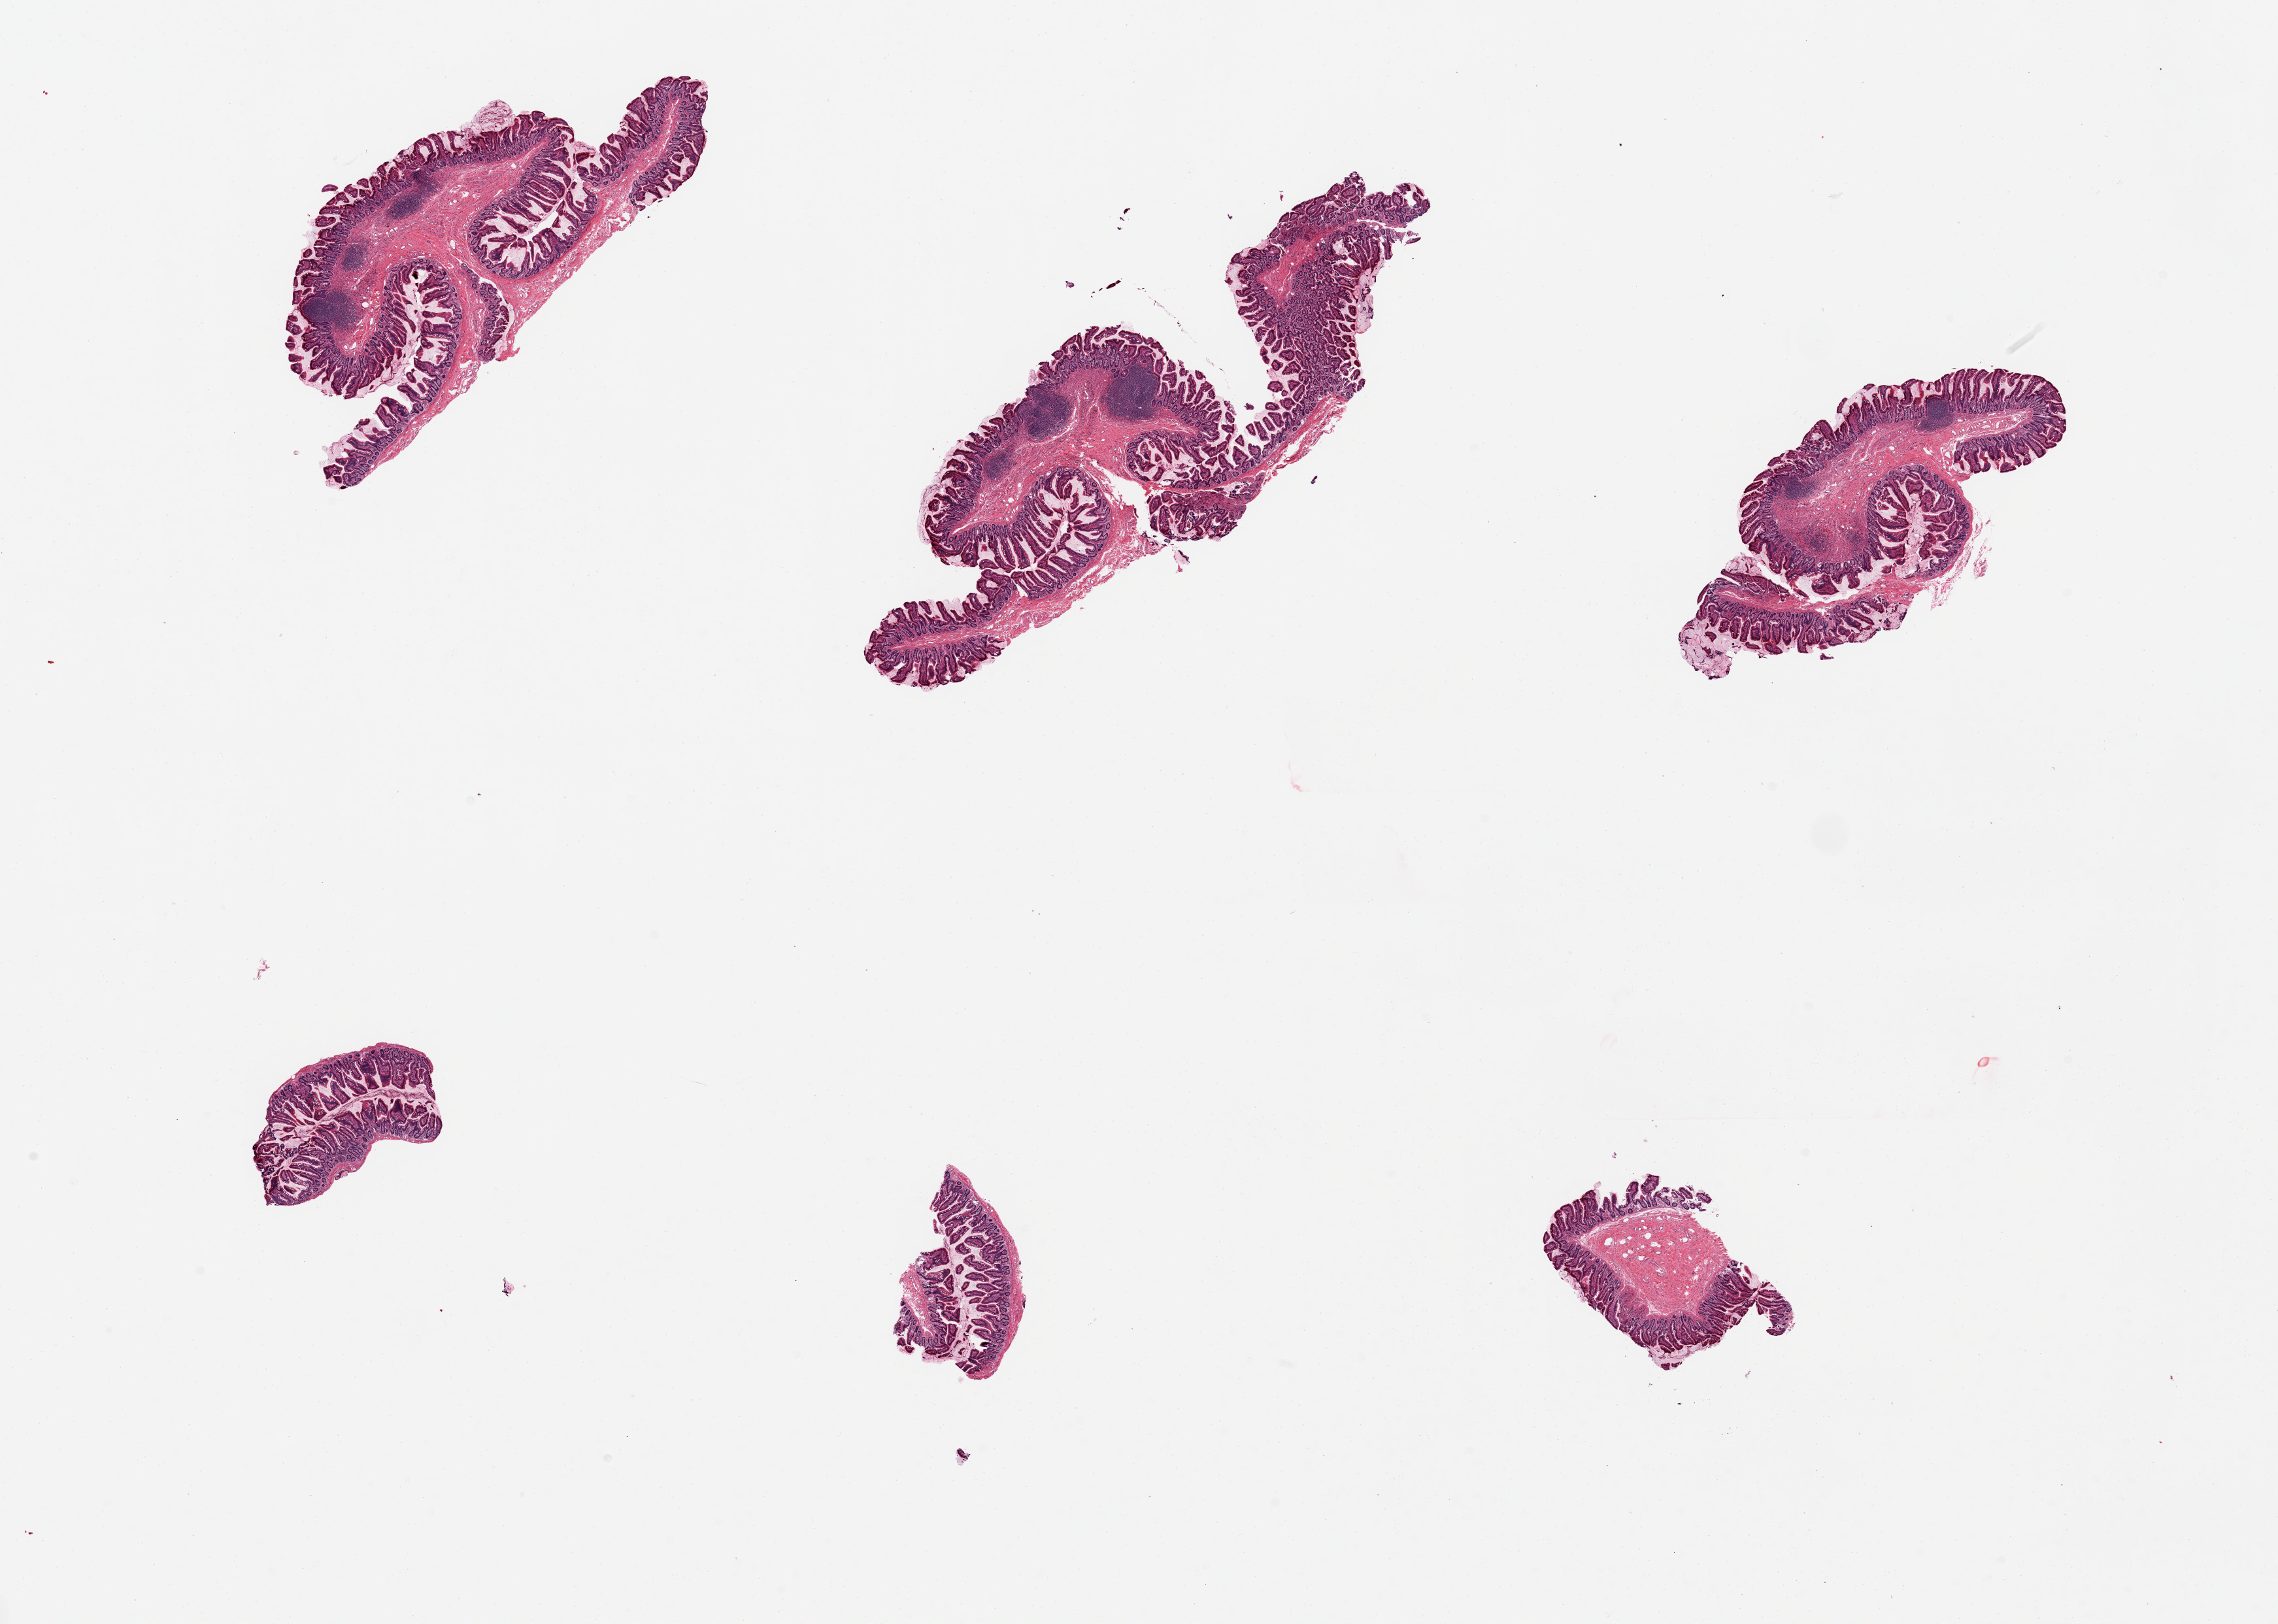
Digitized hematoxylin and eosin (H&E)-stained section — low-resolution overview of the scanned area, about 27.6 x 19.7 mm. PAXgene-fixed, paraffin-embedded tissue. Target tissue: ileum. Tissue donor sample.
• review note (as recorded): 6 pieces of well preserved mucosa with several lymphoid nodules in the 3 largest pieces